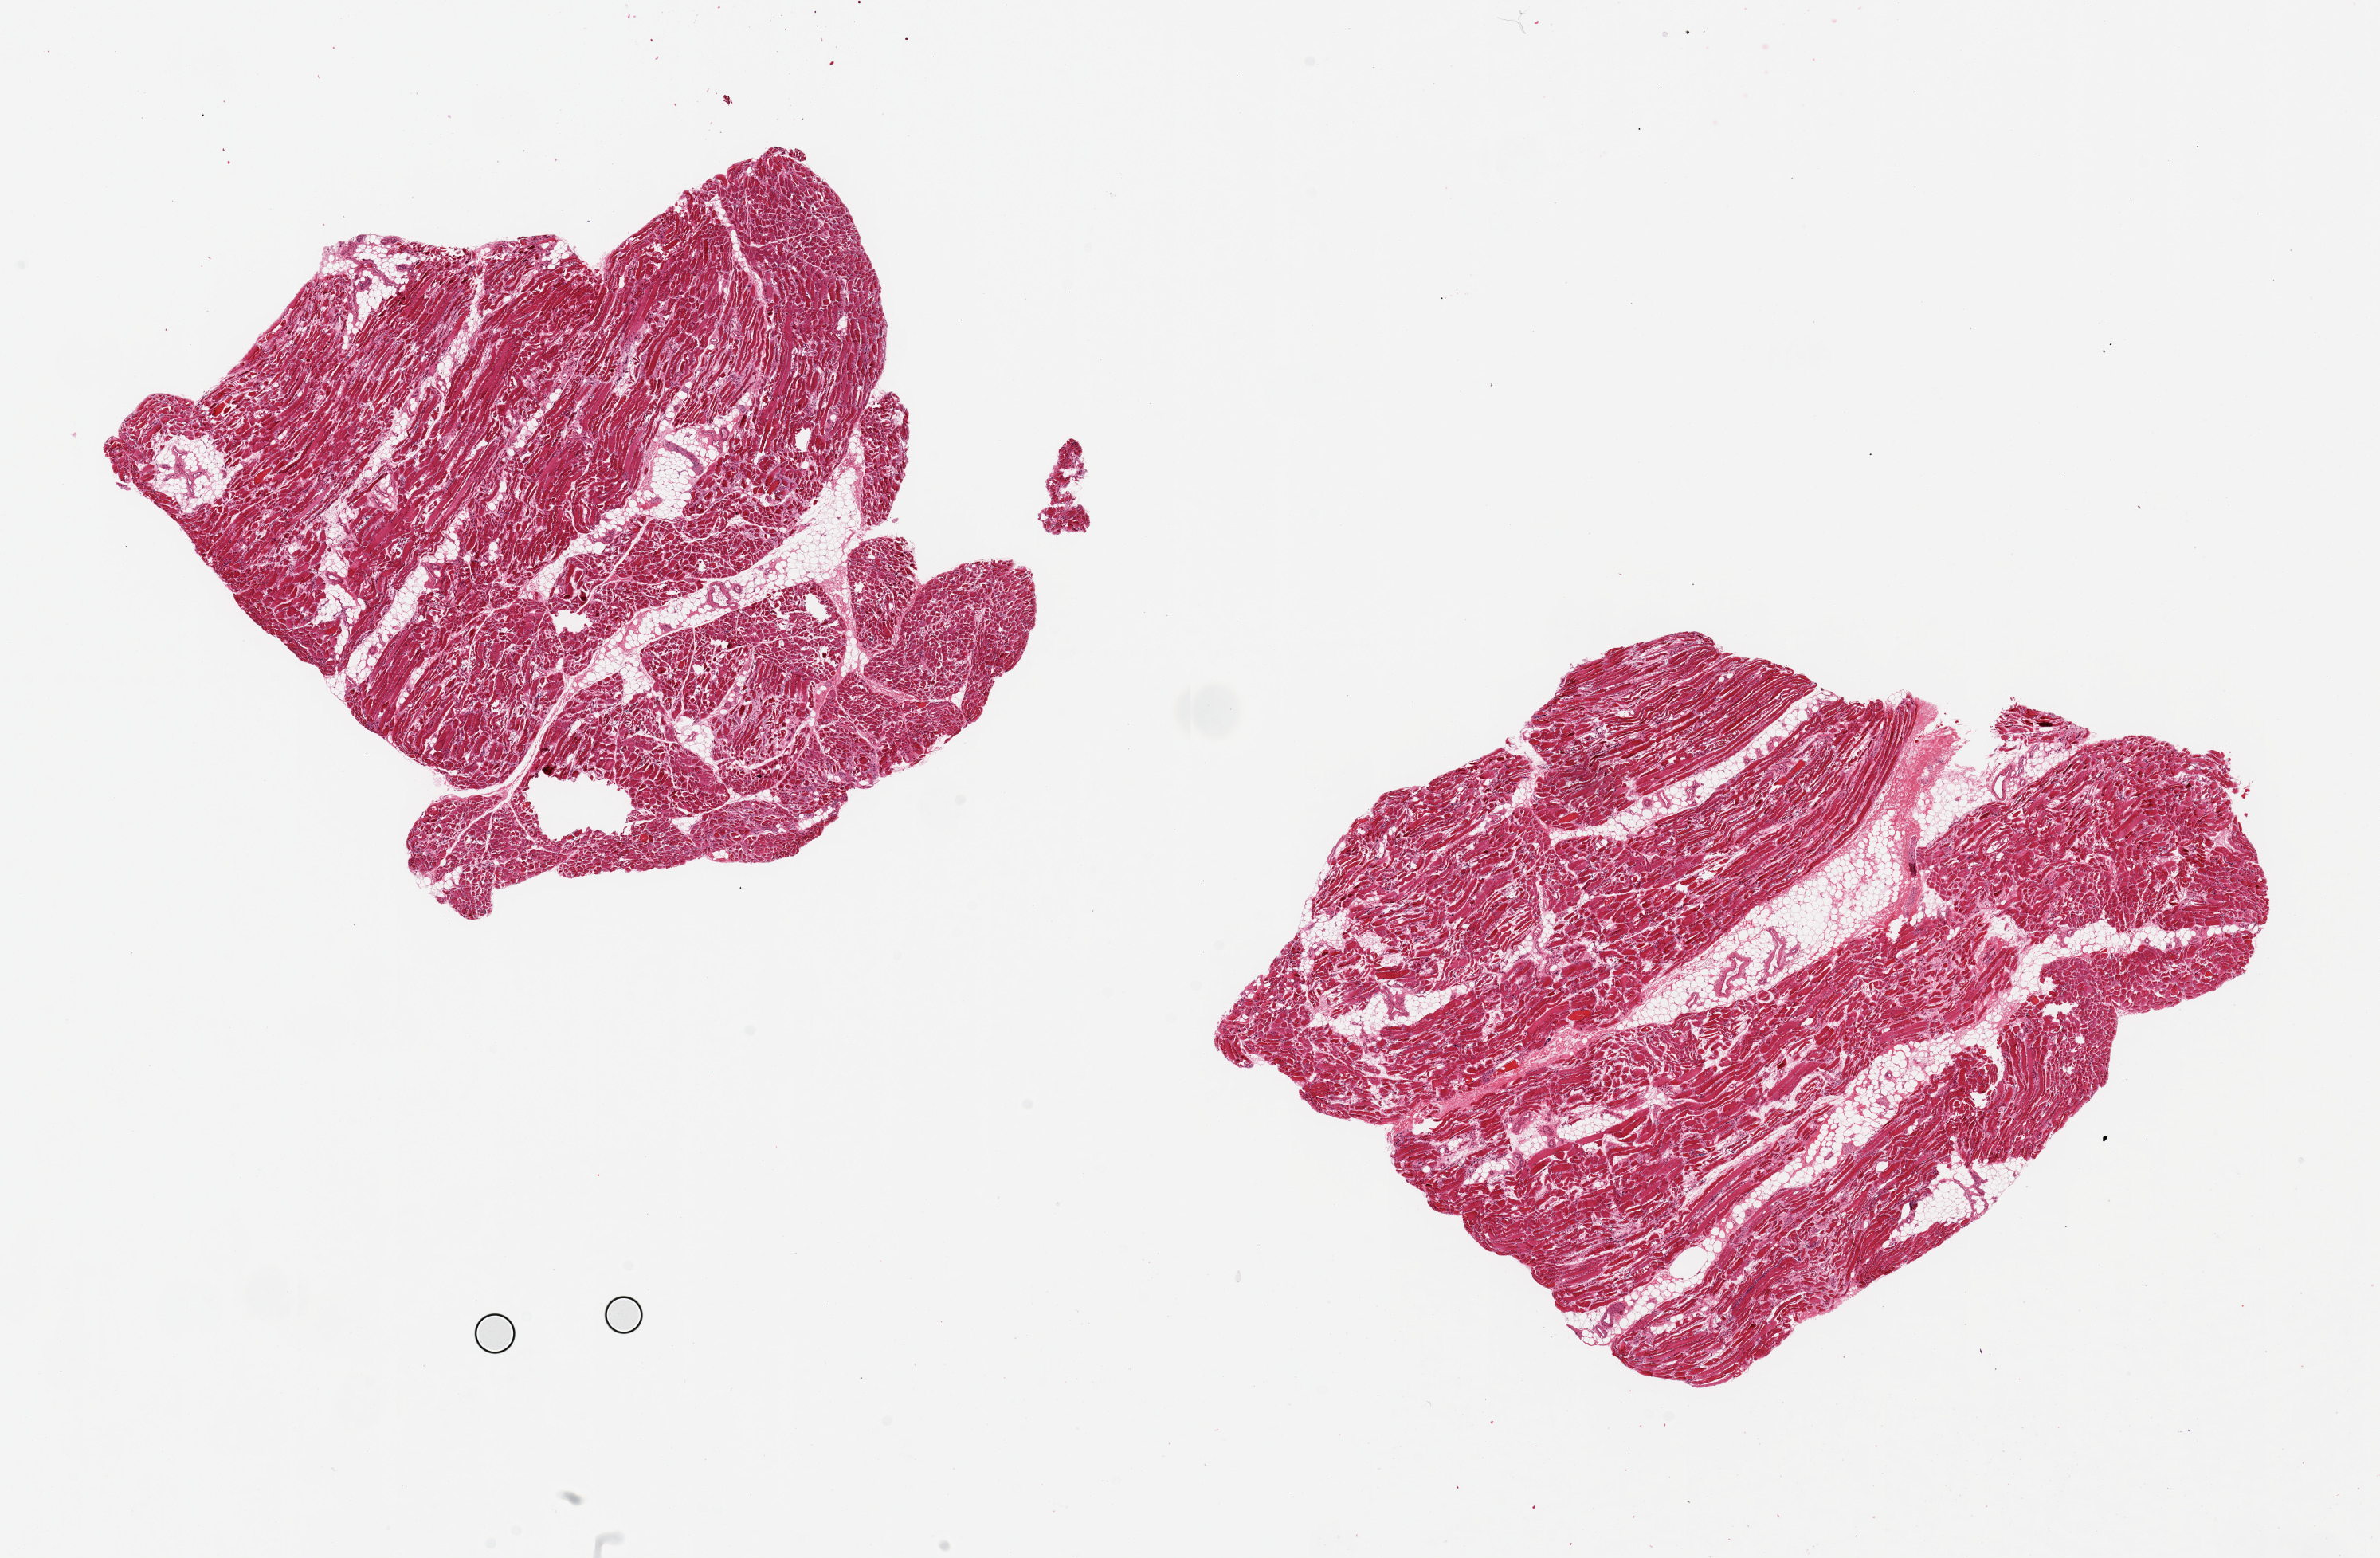
Haematoxylin and eosin whole-slide image, brightfield, a low-resolution overview of the entire scanned area, about 23.6 x 15.5 mm (acquisition: 20x scan); PAXgene-fixed paraffin-embedded (PFPE) section; target tissue: skeletal muscle; tissue donor sample. Donor sex: male.
• review note (as recorded): 2 pieces, 8x8 & 8.5x8mm; moderate atrophy; 20% internal adipose